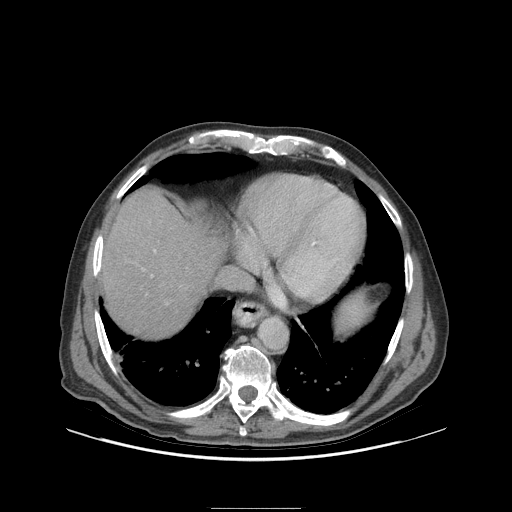
Contrast-enhanced abdominal CT (liver protocol), one axial slice; slice 87 of 105 in the series (ordered by position); reconstruction kernel STANDARD; soft-tissue window (W 400 / L 40 HU); 512 × 512 image matrix. Case-level facts recorded for this patient, not image findings: diagnosis: hepatocellular carcinoma (patient treated with transarterial chemoembolisation; whether this scan precedes or follows treatment is not stated here); TNM stage (as recorded): Stage-I.
Outlined on this slice (semi-automatic segmentation, software-assisted and operator-edited):
- liver parenchyma outside the tumour (the mass and vessels are separate outlines, so this box may not span the whole liver): bounding box <100,188,224,336> (left, top, right, bottom; pixels)
- liver vessels: <151,250,156,277>